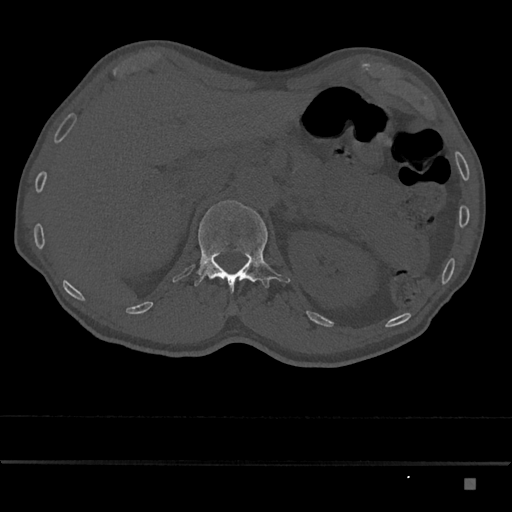
CT including the spine, one axial slice. Bone window (W 1800 / L 400 HU). 512 × 512 image matrix, field of view 390 × 390 mm. Male patient, age 72 years. From the clinical record (not read from this slice): primary cancer: prostate.
Annotated regions visible in this slice (semi-automatically segmented with operator editing):
- L1 vertebra: bounding box (x1, y1, x2, y2) in pixels: (194, 200, 290, 294)